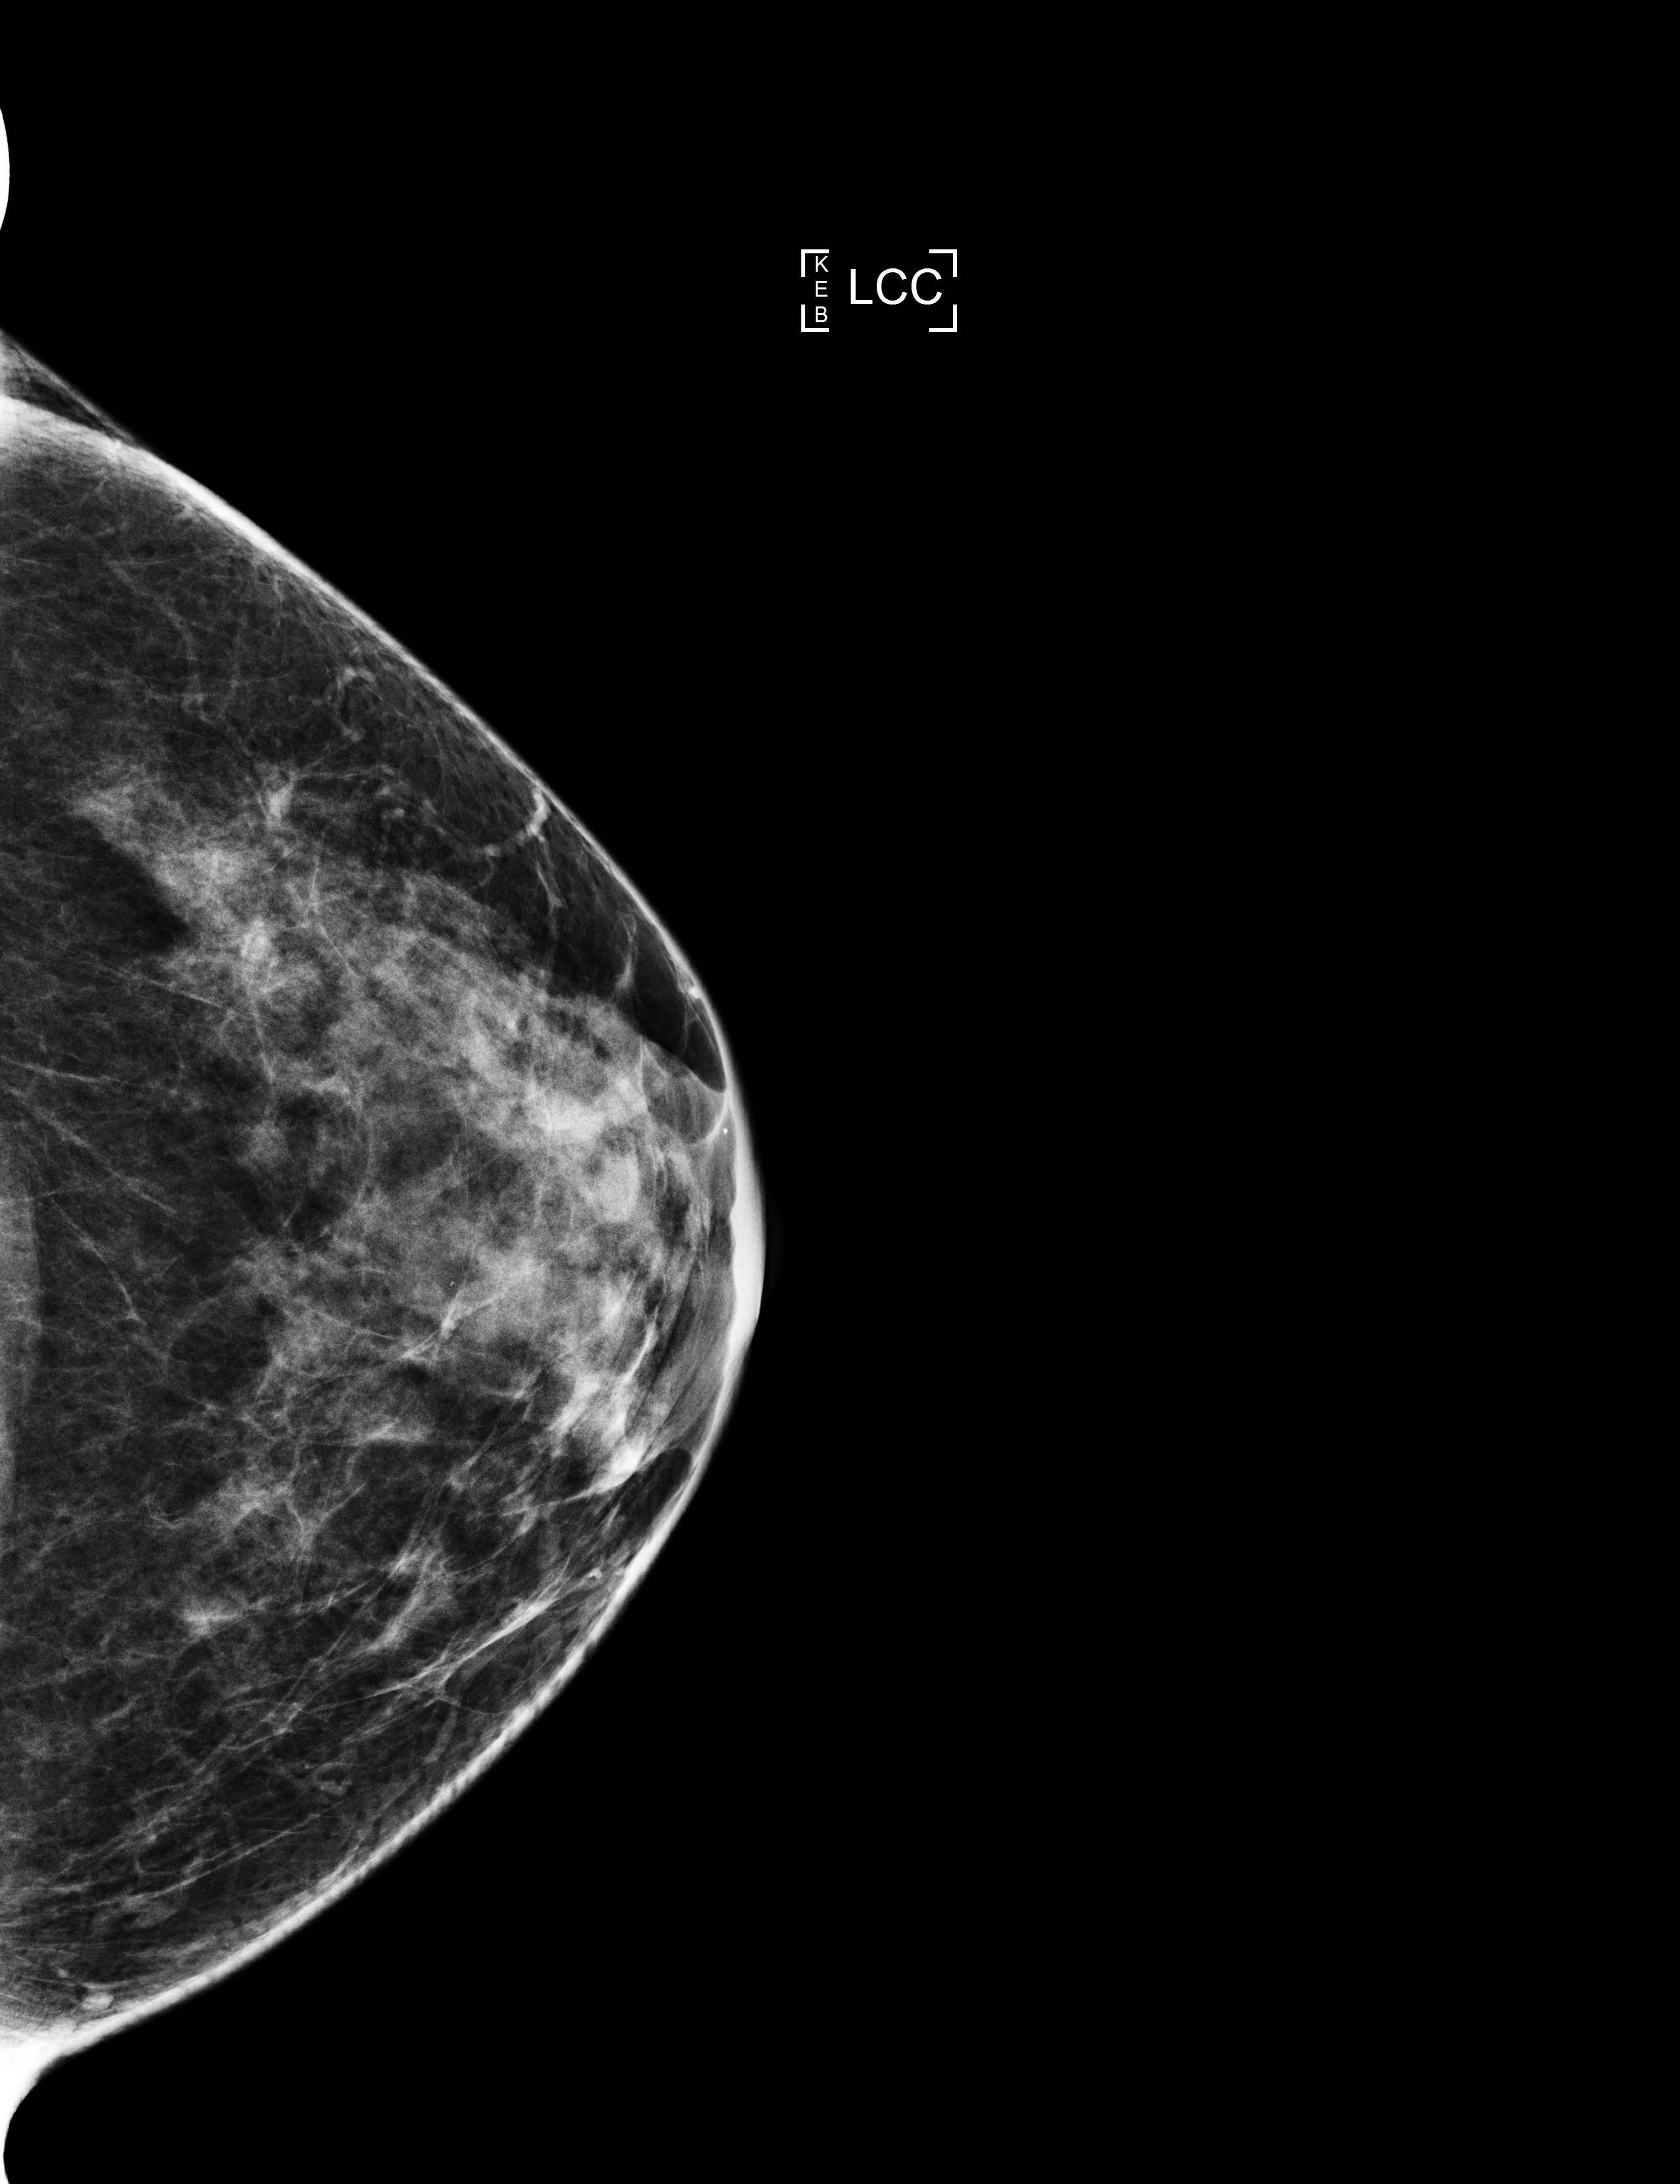
Digital mammogram (FFDM); left breast; craniocaudal (CC) view; annual screening mammography examination; compressed breast thickness 50 mm; system: Selenia Dimensions. Patient: female, 44 years.
- BI-RADS breast density category at the screening exam (both breasts, scale 1–4): 3
- final BI-RADS category for the screening round (tomosynthesis exam, both breasts): category 2
- recall: no recall after this screen